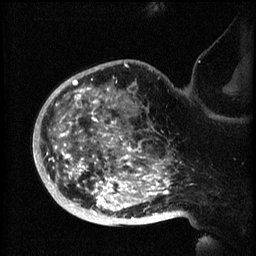
Breast MRI (dynamic contrast-enhanced), one sagittal slice; slice 45 of 60 in the series (ordered by position); 3 images stored at this slice position (order not interpretable as contrast timing); 1.5 T; TE 4.2 ms, TR 8.2 ms; 2 mm slice thickness; 256 × 256 image matrix. Patient: female, 50 years.
Annotated regions visible in this slice (semi-automatically segmented with operator editing):
- analysis volume of interest (the breast-tissue region the enhancement analysis was run in; not a lesion): bounding box (x1, y1, x2, y2) in pixels: (44, 72, 173, 219)
- tumour enhancement mask (voxels above the 70 % enhancement threshold inside the analysis volume of interest): (47, 80, 173, 219)